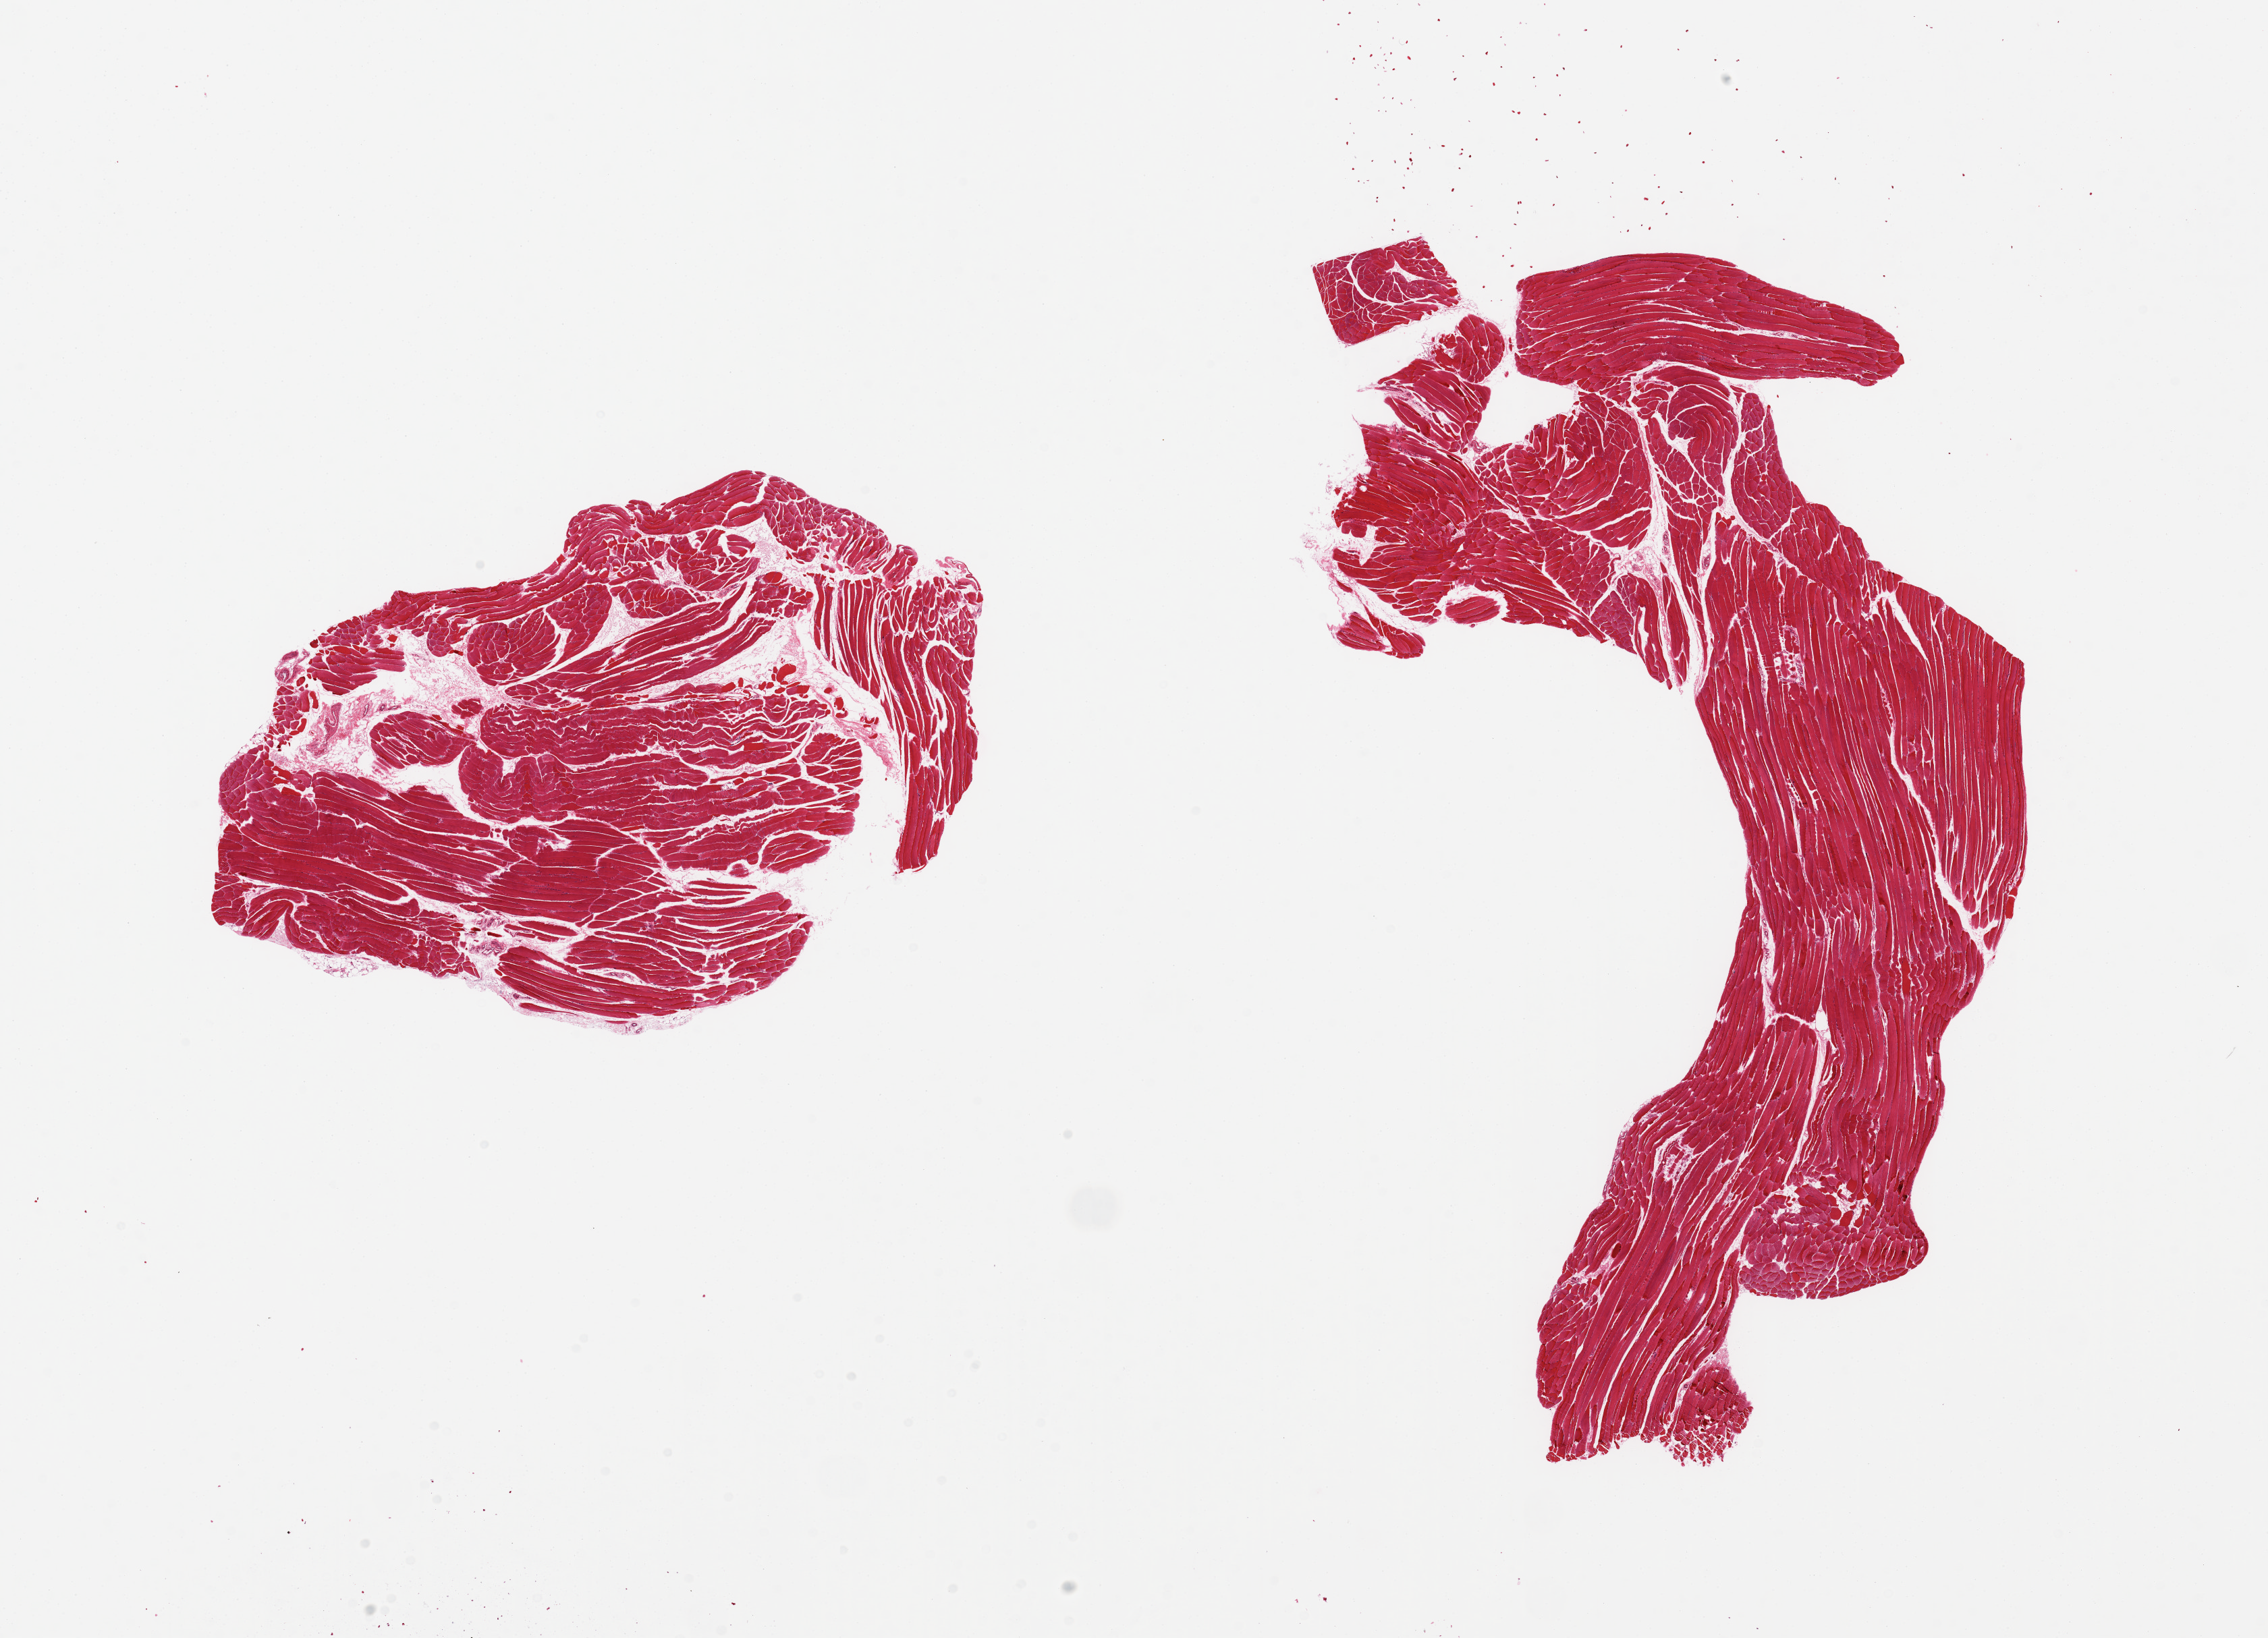
Whole-slide image, hematoxylin and eosin (H&E) stain, whole scanned area (about 26.6 x 19.2 mm) shown as a low-resolution overview, PAXgene-fixed, paraffin-embedded tissue, section of skeletal muscle (target tissue), donor tissue sample. Donor sex: female.
Review note (as recorded): 2 pieces, ~10% interstitial fat.